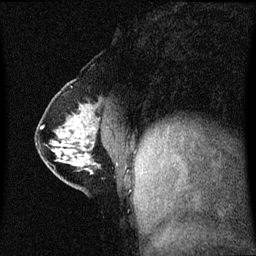
Breast MRI (dynamic contrast-enhanced), one sagittal slice; position 22 of 60 along the scan axis; dynamic contrast-enhanced series, image 2 of 3 at this slice position (ordered by acquisition); 1.5 T; TE 4.2 ms, TR 8.4 ms; 2 mm slice thickness; 256 × 256 image matrix, field of view 210 × 210 mm. Patient: female, 40 years. Case-level facts recorded for this patient, not image findings: setting: breast cancer imaged before/during neoadjuvant chemotherapy; receptor status: triple-negative.
Structures marked on this image (semi-automatic segmentation, software-assisted and operator-edited):
- analysis volume of interest (the breast-tissue region the enhancement analysis was run in; not a lesion): bounding box [x1, y1, x2, y2] px = [37, 112, 118, 188]
- tumour enhancement mask (voxels above the 70 % enhancement threshold inside the analysis volume of interest): [61, 135, 65, 138]